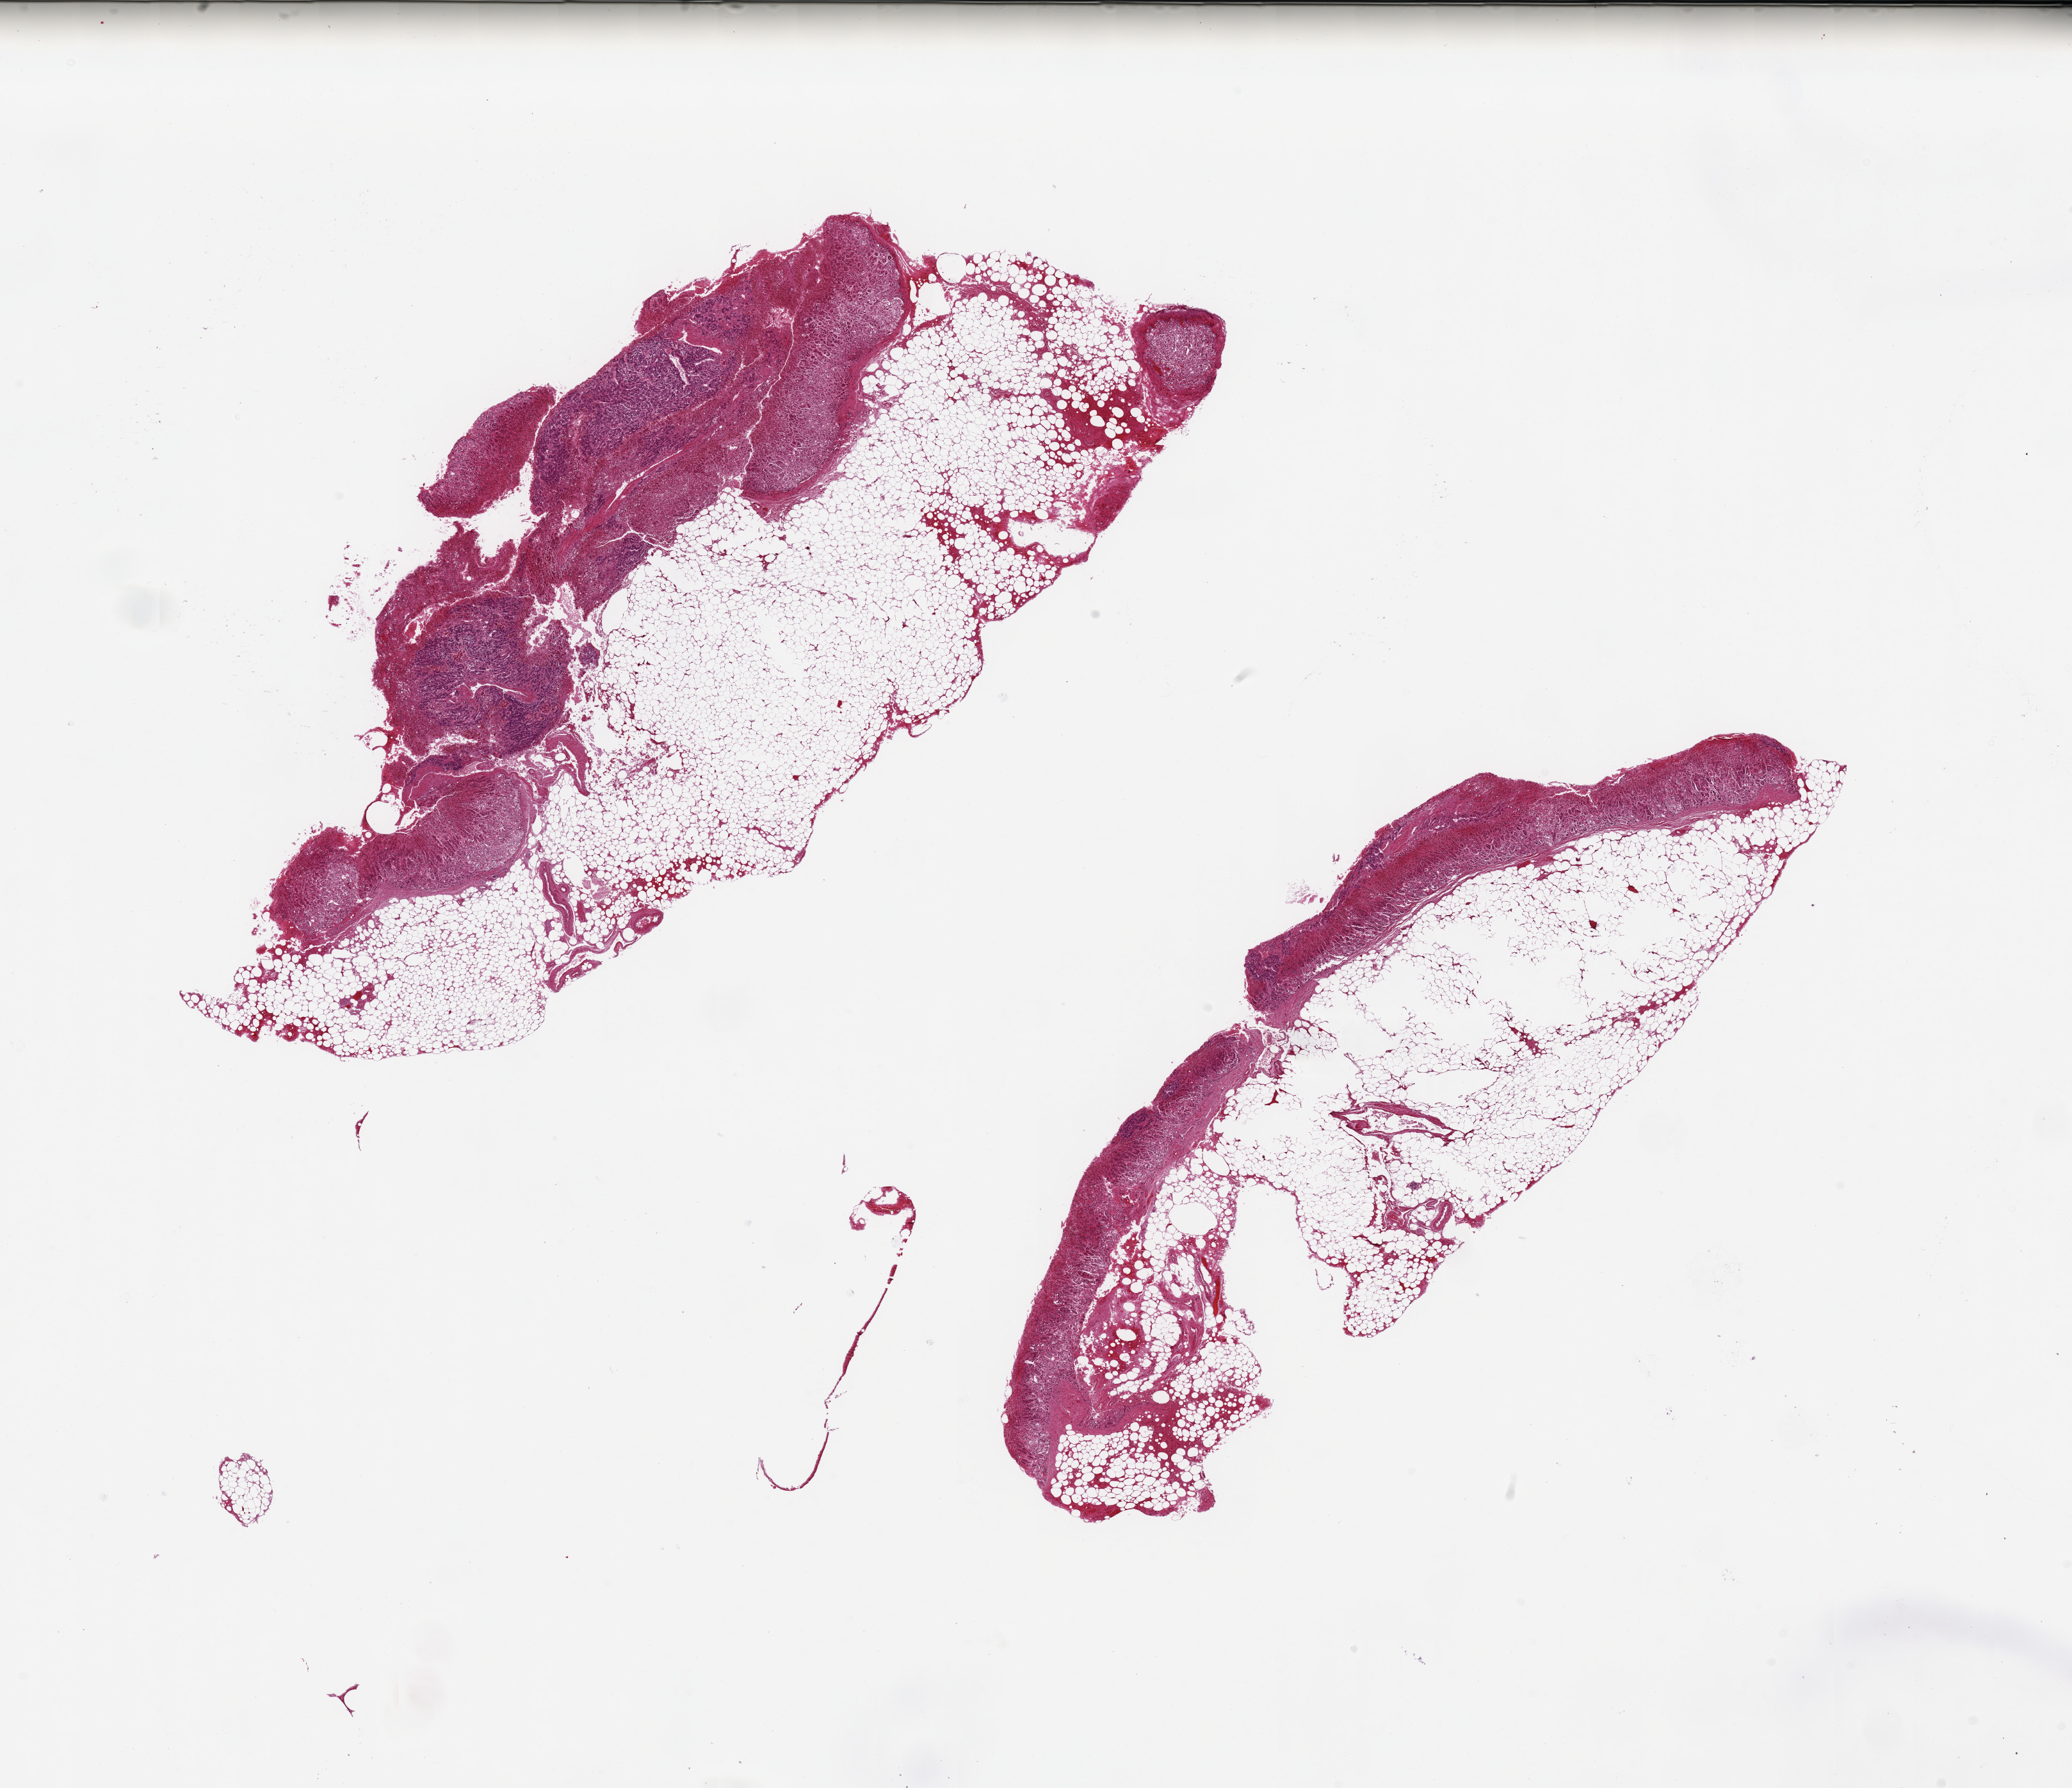
Hematoxylin and eosin (H&E) whole-slide image — low-resolution overview of the scanned area, about 25.6 x 22.1 mm. Male donor.
Specimen: PAXgene-fixed paraffin-embedded (PFPE) section; sampled site (target tissue): adrenal gland; donor tissue sample.